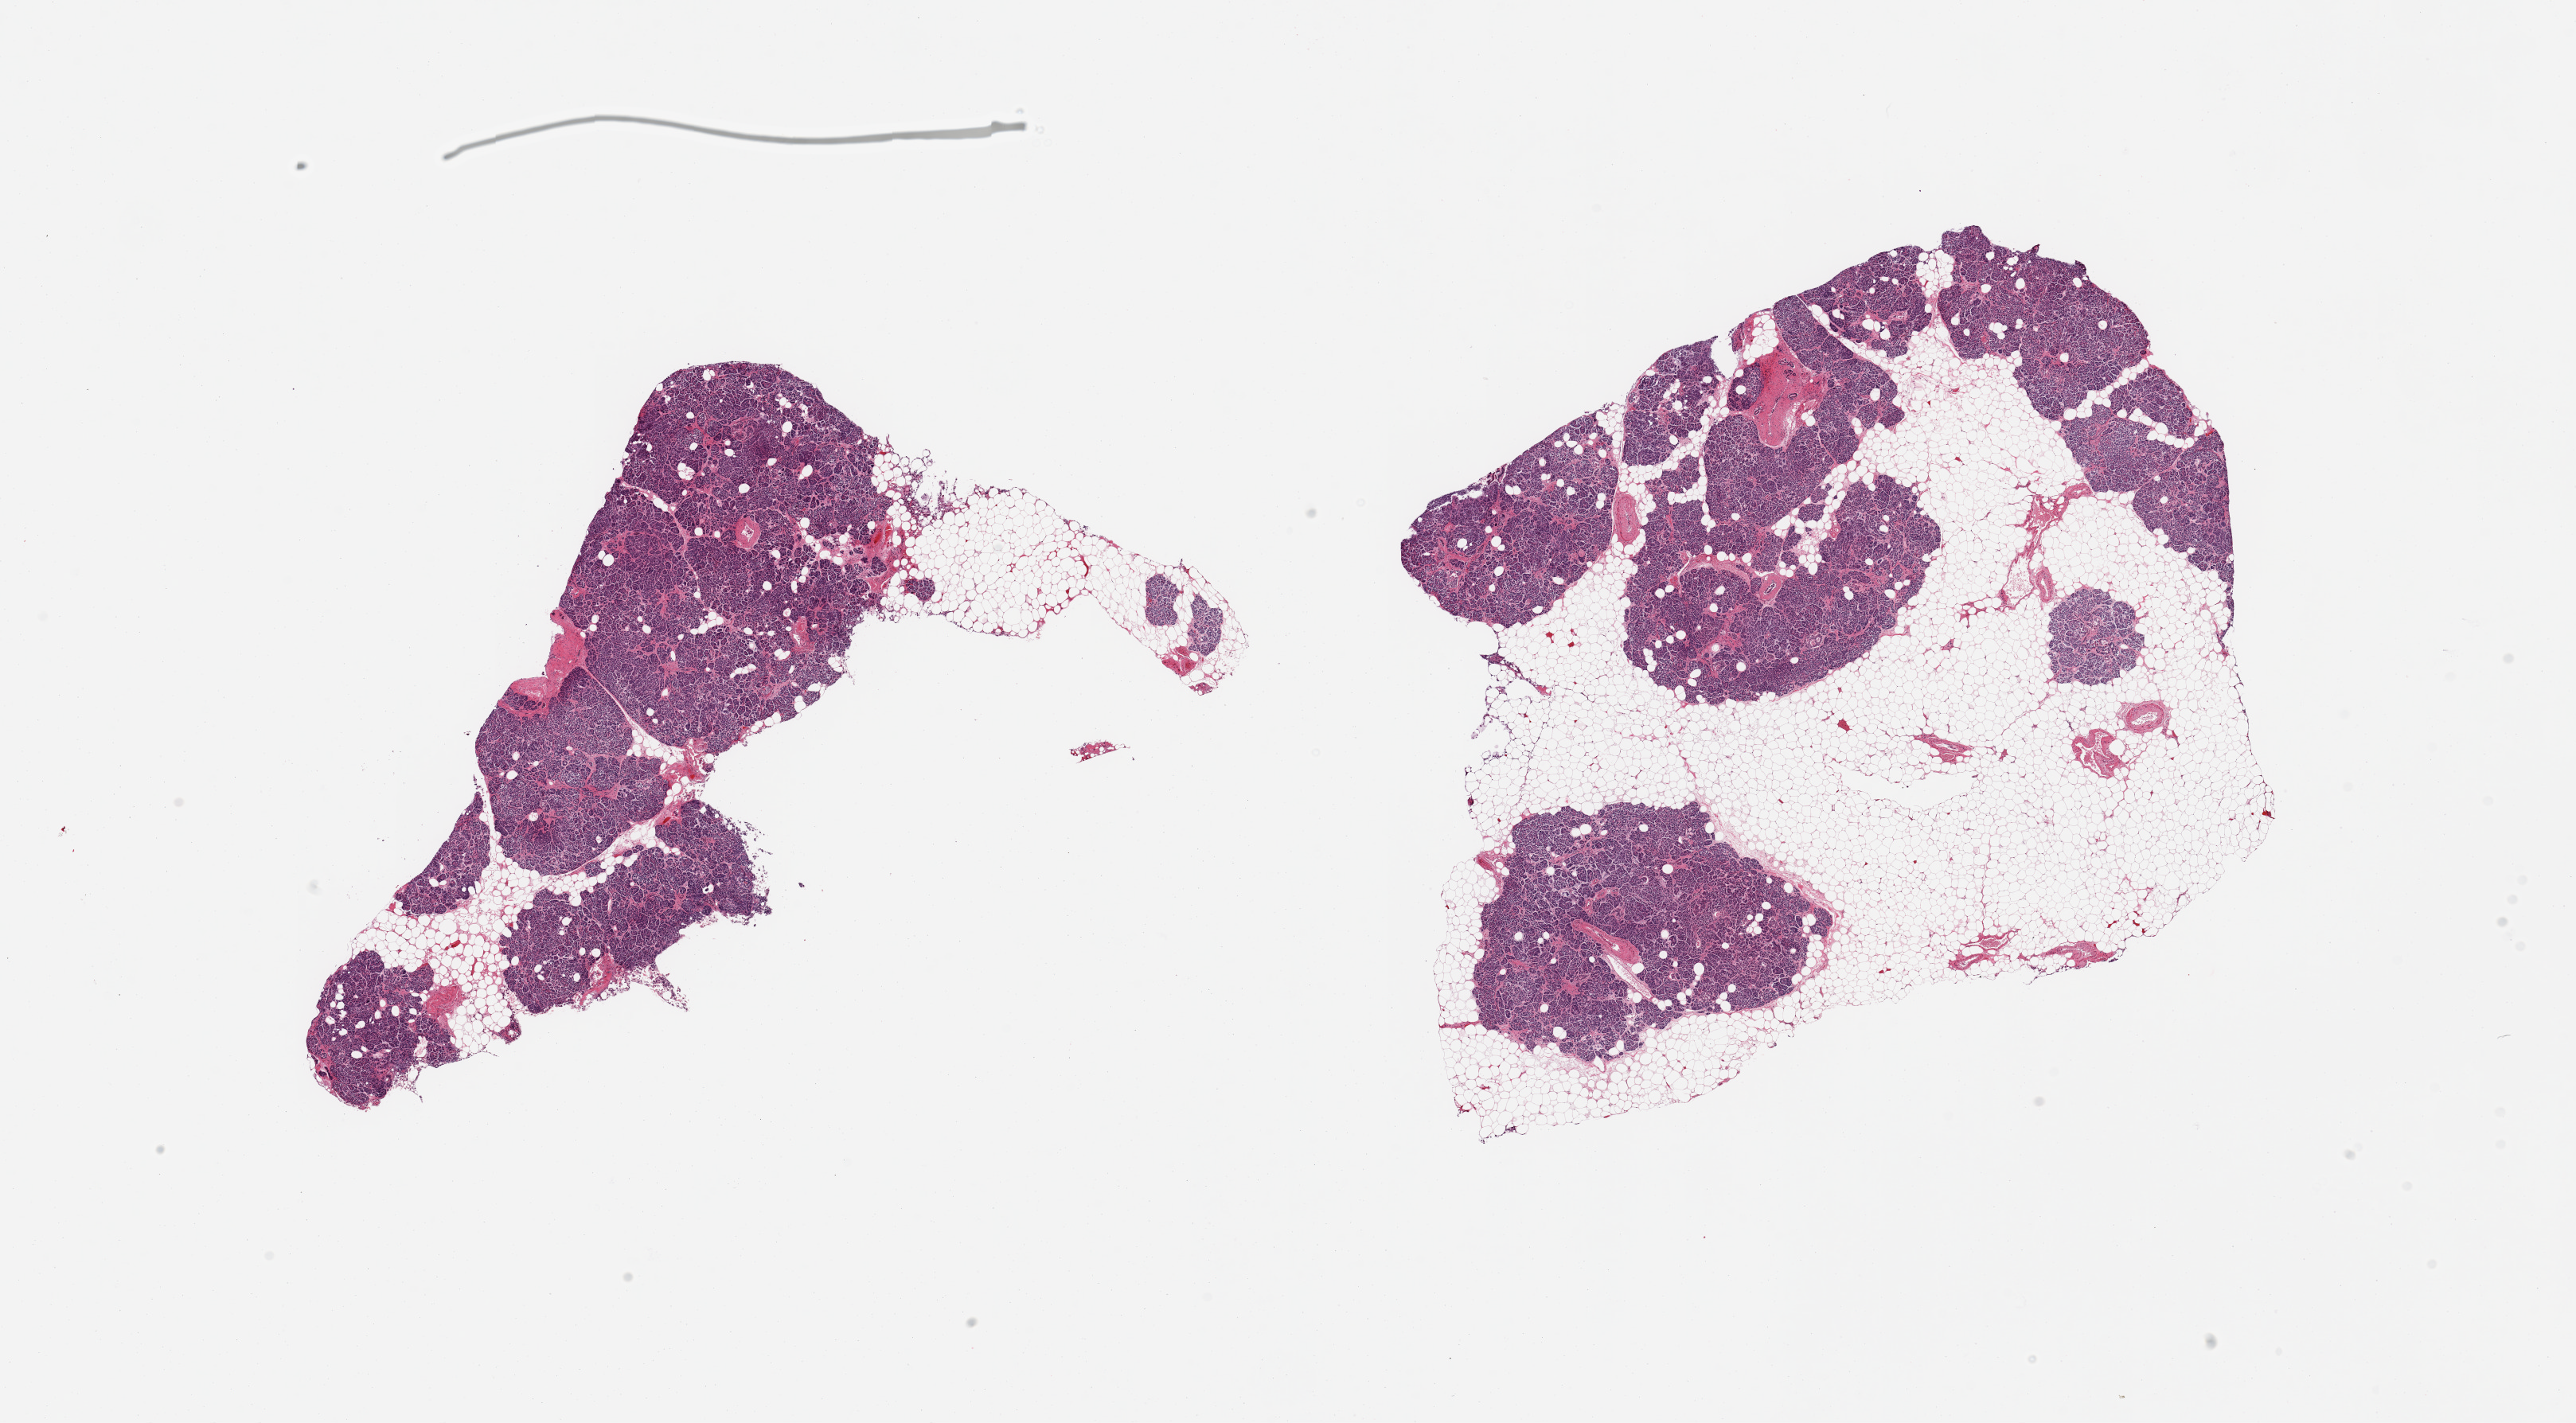
Whole-slide image, H&E stain — whole scanned area (about 25.6 x 14.1 mm, slide scanned at 20x) shown as a low-resolution overview. PAXgene-fixed paraffin-embedded (PFPE) section. Sampled site (target tissue): pancreas. Donor tissue sample.
- pathologist's review note for this sample: 2 pieces, moderate saponification; Islets dimly visible, a few, but degrading; ~40% adherent/interstitial fat